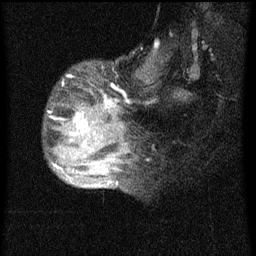
Breast MRI (dynamic contrast-enhanced), one sagittal slice; position 19 of 60 along the scan axis; dynamic contrast-enhanced series, image 2 of 4 at this slice position (ordered by acquisition); 1.5 T; TE 4.2 ms, TR 8 ms; 2 mm slice thickness; 256 × 256 image matrix. Female patient, age 50 years.
Structures marked on this image (semi-automatic segmentation, software-assisted and operator-edited):
- analysis volume of interest (the breast-tissue region the enhancement analysis was run in; not a lesion): box from (x=46, y=68) to (x=124, y=177) px
- tumour enhancement mask (voxels above the 70 % enhancement threshold inside the analysis volume of interest): (x=55, y=100)–(x=116, y=167)